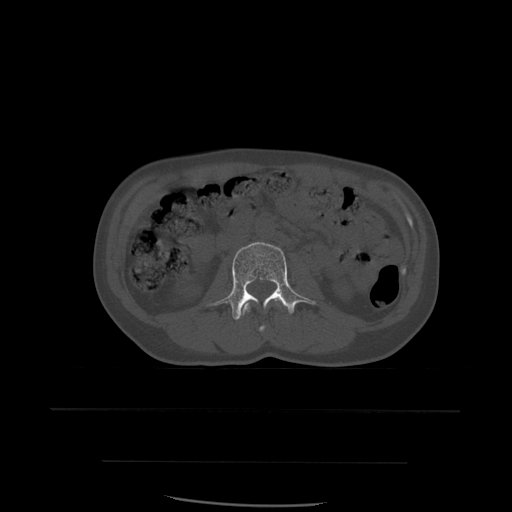
CT including the spine, one axial slice. Slice 203 of 574 in the series (ordered by position). Bone window (W 1800 / L 400 HU). 1.25 mm slice thickness. 512 × 512 image matrix, field of view 392 × 392 mm. Patient age 48 years. Case-level facts recorded for this patient, not image findings: primary cancer: lung; vertebrae with lytic lesions (as recorded): T11.
Outlined on this slice (semi-automatic segmentation, software-assisted and operator-edited):
- L2 vertebra: bounding box <241,299,282,333> (left, top, right, bottom; pixels)
- L3 vertebra: <213,242,316,321>